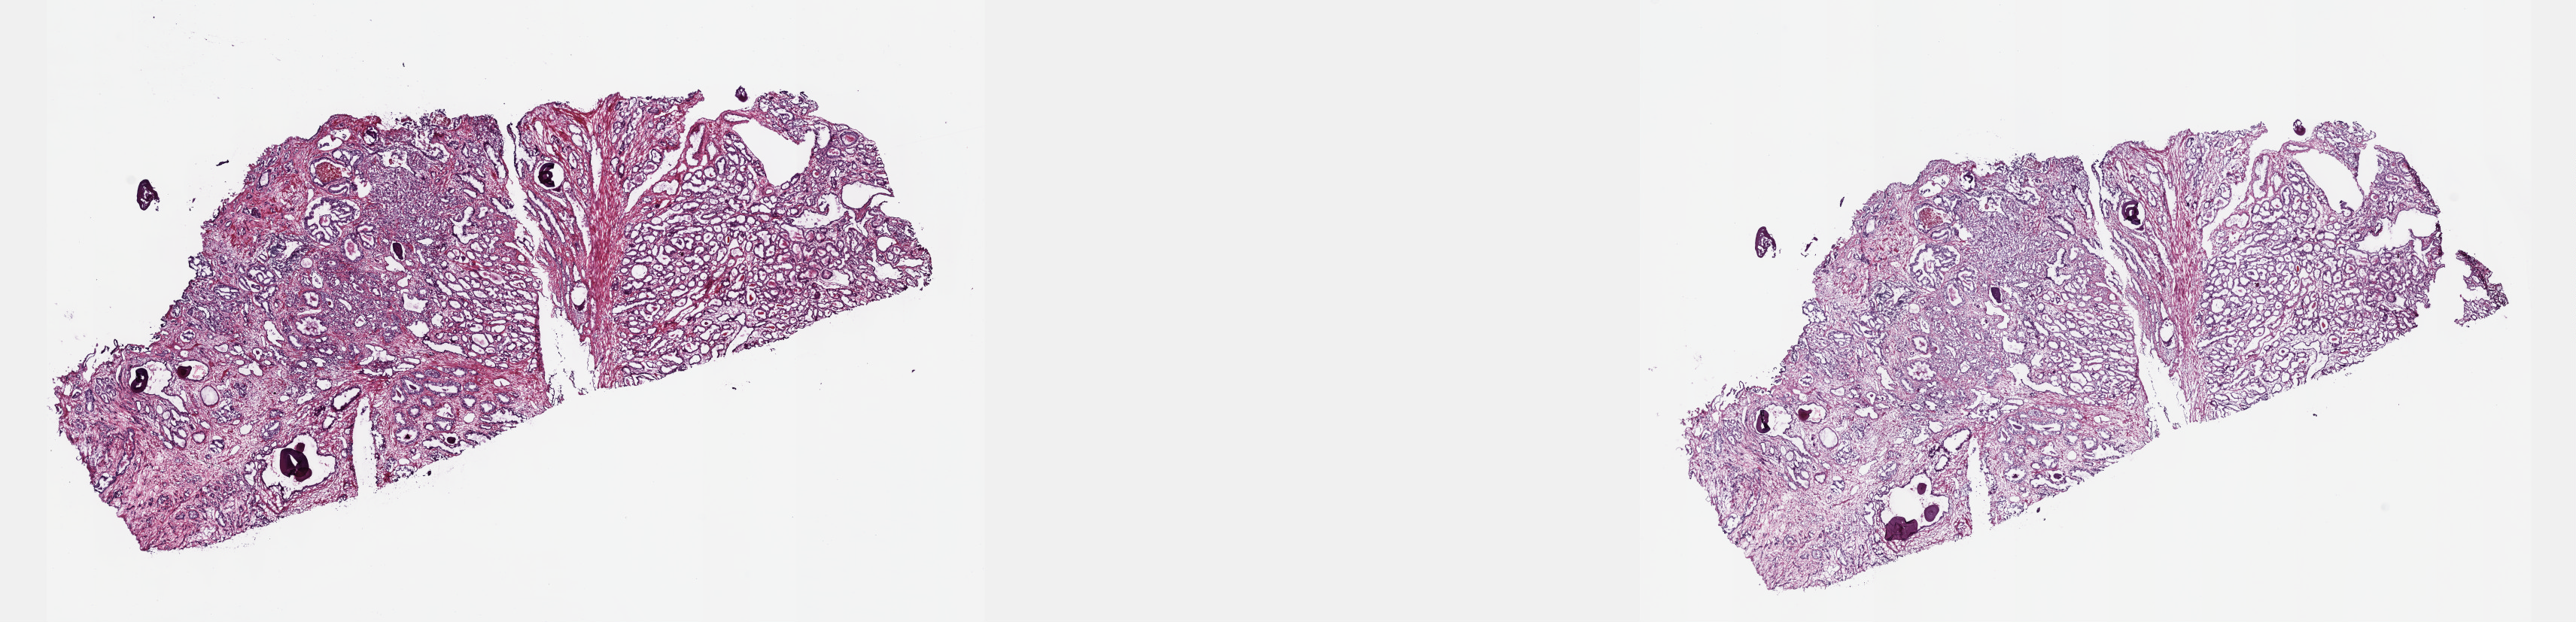
Whole-slide histology image, Hematoxylin and eosin (H&E) stained — whole scanned area (about 27.7 x 6.7 mm) shown as a low-resolution overview. Frozen section from the top of the tissue portion. Prostate, primary tumour sample. Male, age 56 years at initial diagnosis. Gleason score: 8 (3+5). Pathologist review of this section (percent, as recorded): tumour cells 80%, tumour nuclei 90%, normal cells 0%, stromal cells 20%, necrosis 0%. Inflammatory infiltration, as recorded: lymphocyte infiltration 0%, monocyte infiltration 0%, neutrophil infiltration 0%.
Lymph nodes positive (case pathology): 0 of 8 examined. Laterality: bilateral. Pathologic diagnosis: Adenocarcinoma, NOS (prostate gland).